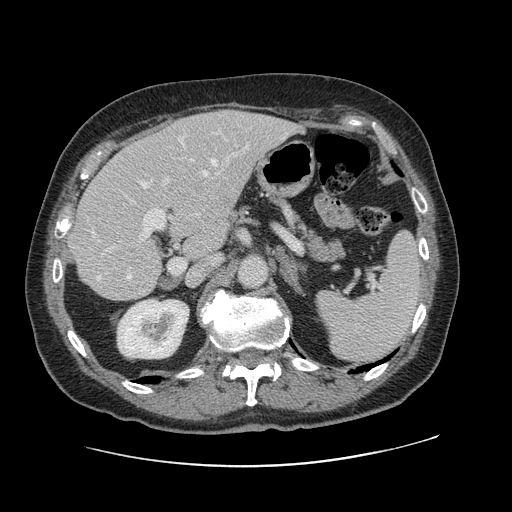
Contrast-enhanced abdominal CT, one axial slice; position 68 of 138 along the scan axis; 120 kVp; intravenous contrast given; soft-tissue window (W 400 / L 40 HU); 2.5 mm slice thickness; 512 × 512 image matrix, field of view 402 × 402 mm. Male patient, age 71 years. From the clinical record (not read from this slice): diagnosis: colorectal cancer liver metastases, imaged before liver resection; multiple liver metastases: no; largest metastasis: 3.3 cm; chemotherapy before resection: no.
Outlined on this slice (outlined manually by an expert reader):
- hepatic veins: bounding box (x1, y1, x2, y2) in pixels: (92, 141, 223, 281)
- liver: (72, 111, 296, 300)
- planned liver remnant (the part of the liver to remain after resection): (71, 145, 223, 300)
- portal vein (with intrahepatic branches): (101, 143, 249, 274)
- liver metastasis: (221, 195, 231, 205)